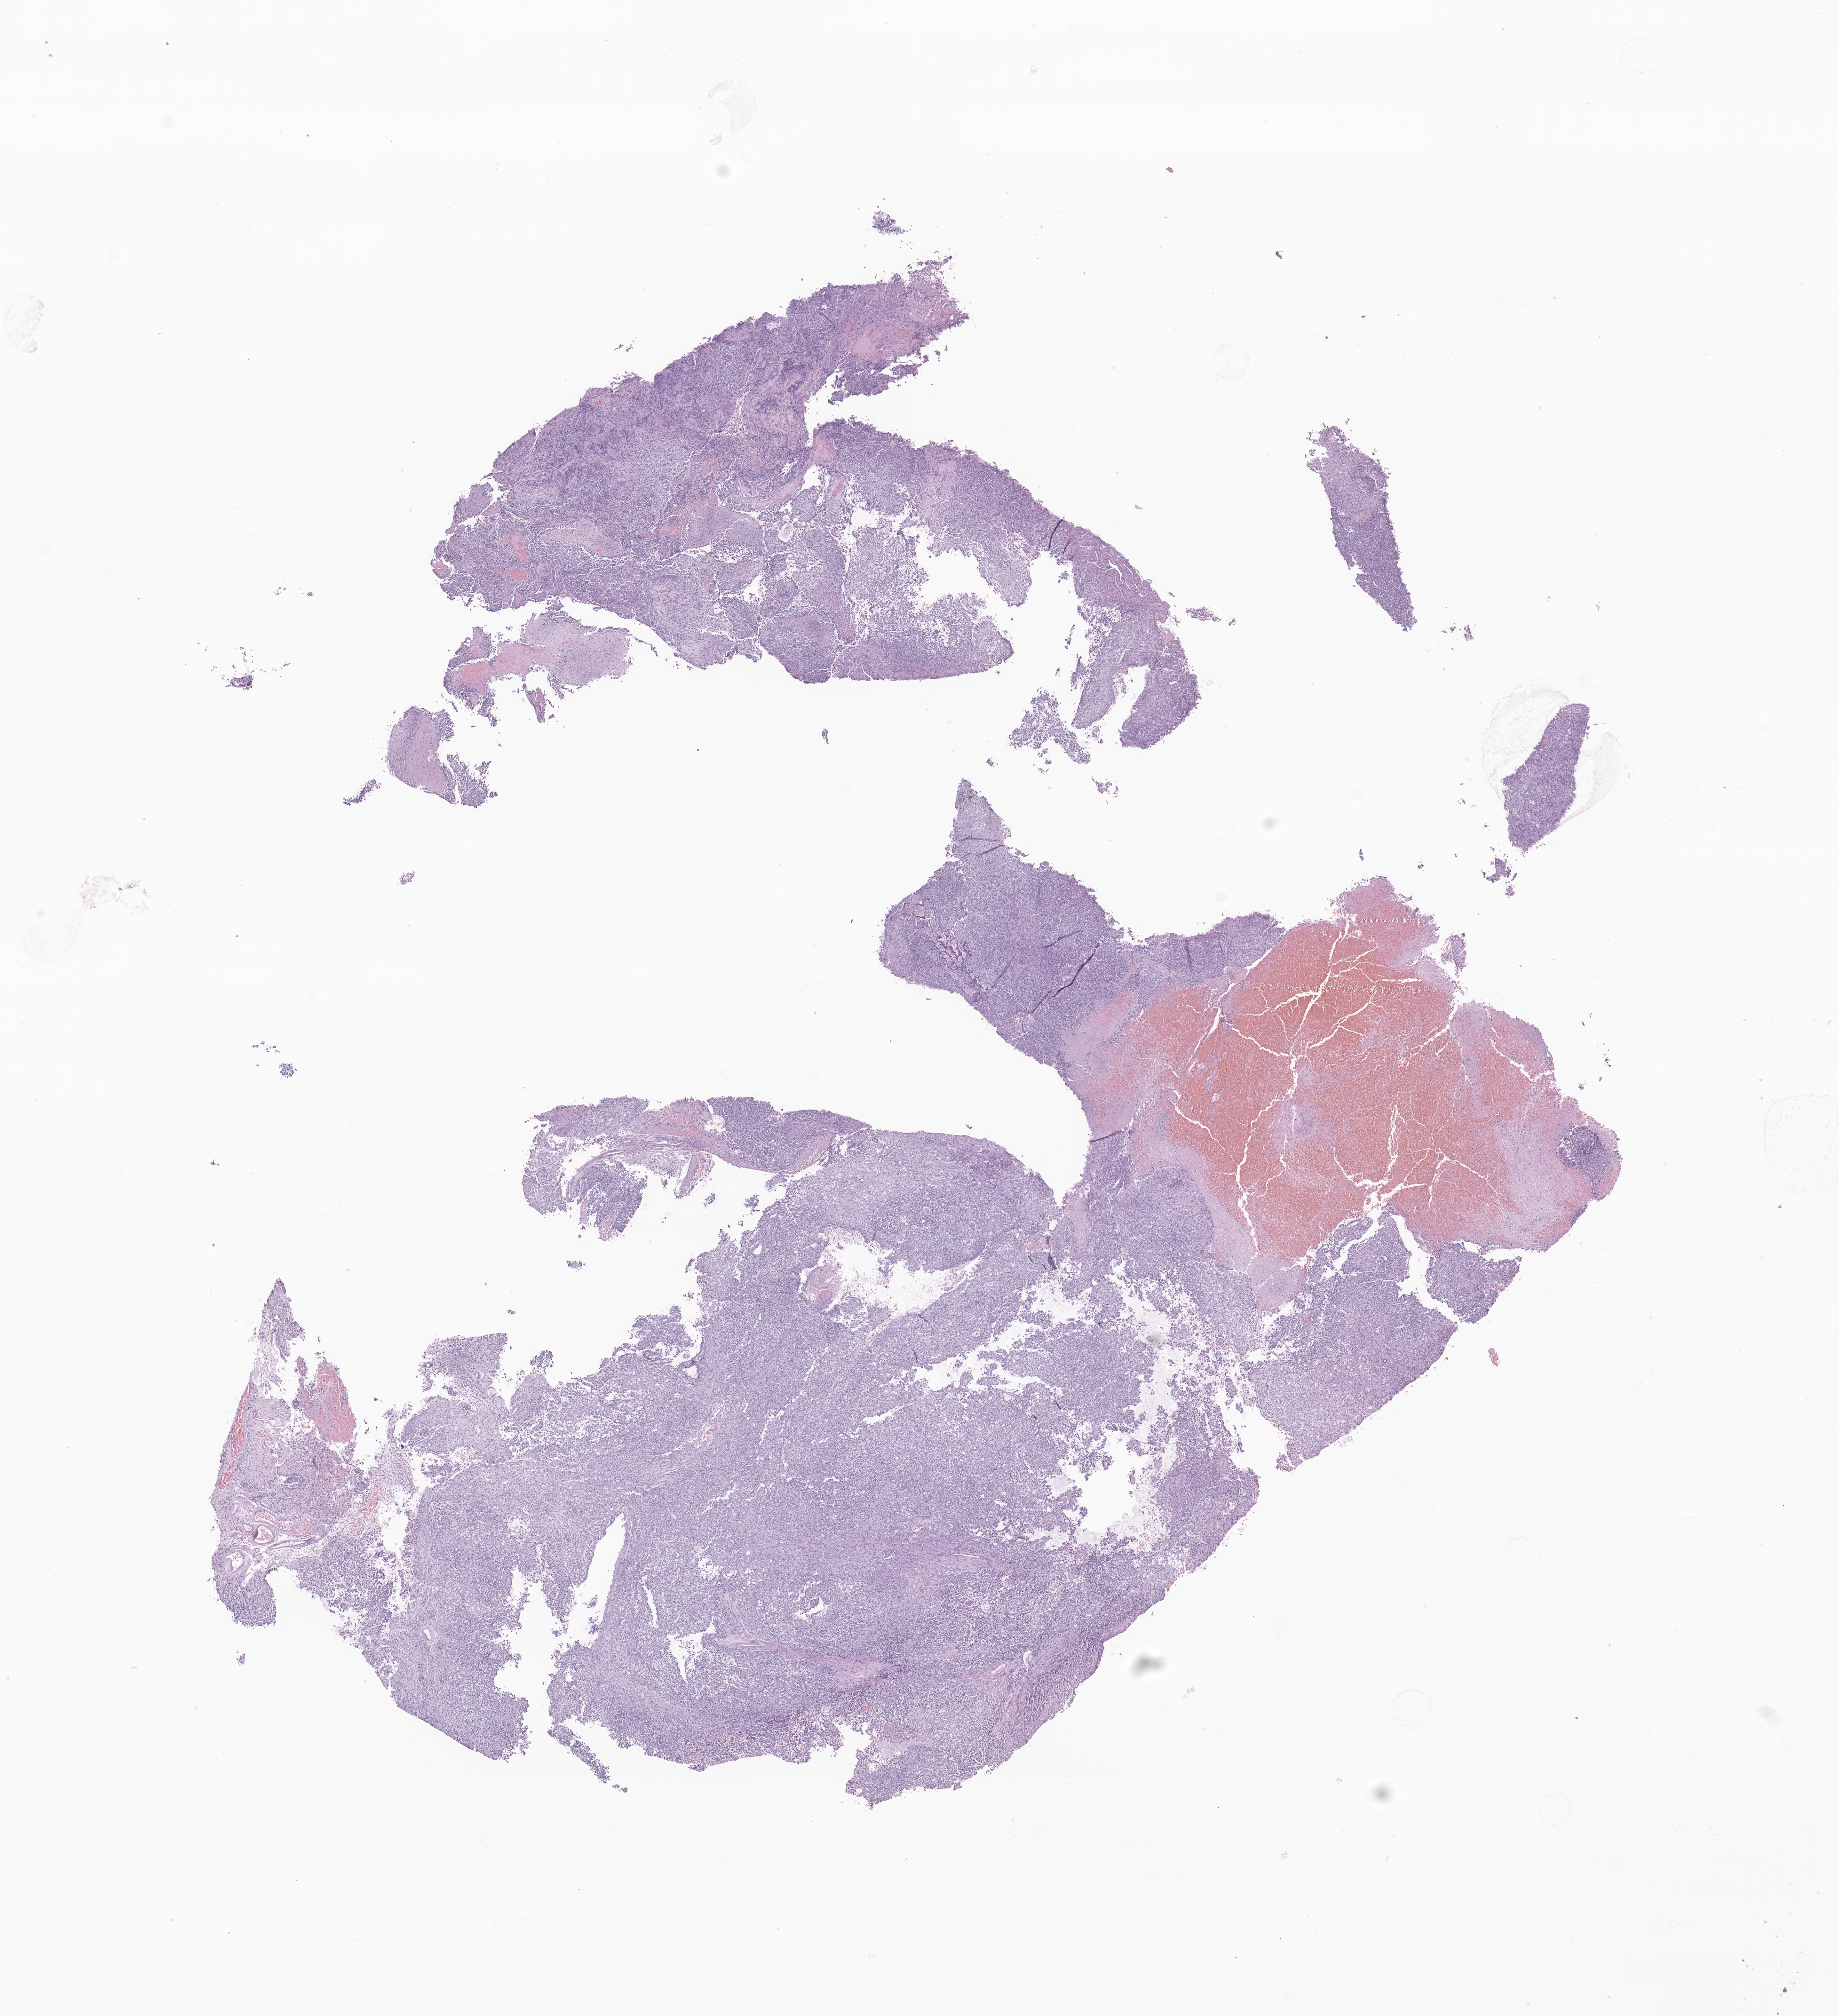
Whole-slide image, hematoxylin and eosin (H&E) stain of tumor tissue from the brain — a low-resolution overview of the entire scanned area, about 16.5 x 18.1 mm; formalin-fixed, paraffin-embedded (FFPE) tissue. Patient male; age 663 days (about 1.8 years).
Recorded diagnosis: Atypical teratoid/rhabdoid tumor.